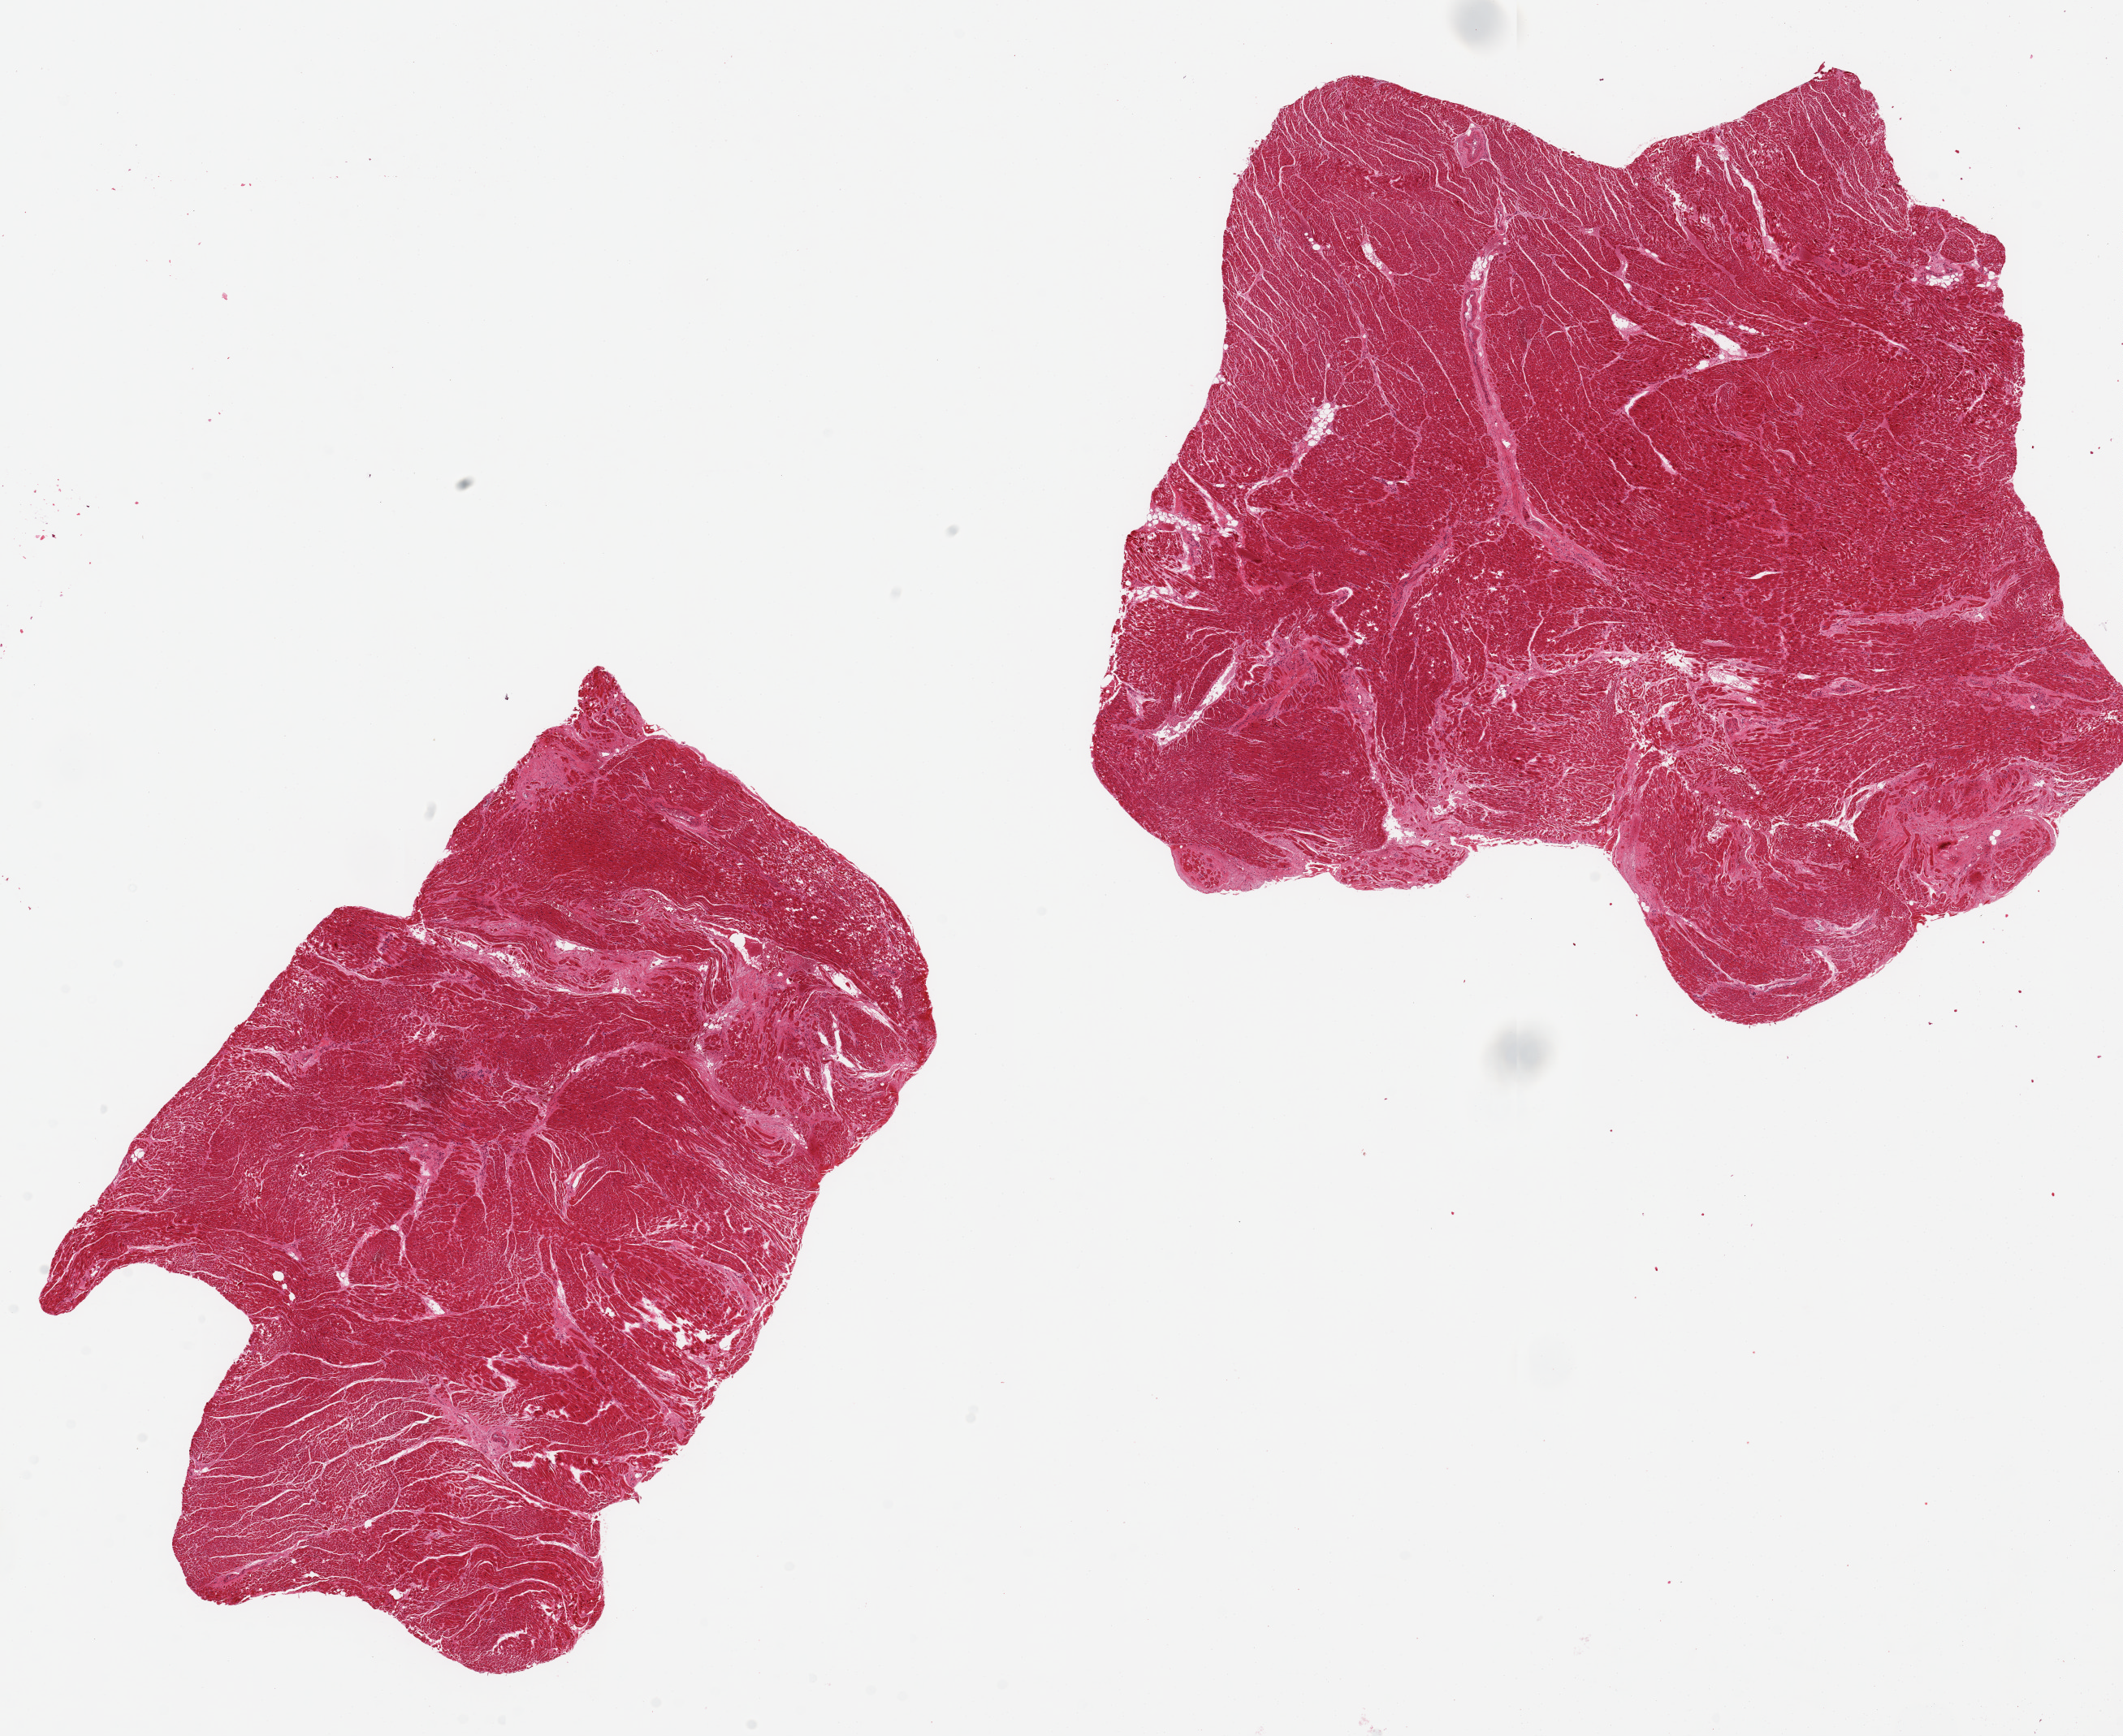
Whole-slide image, H&E stain — whole scanned area (about 20.7 x 16.9 mm) shown as a low-resolution overview, PAXgene-fixed, paraffin-embedded tissue, sampled site (target tissue): heart, donor tissue sample.
Pathologist's review note for this sample: 2 aliquots ~8x7mm. Focal healed infarct, ~1.5mm d.